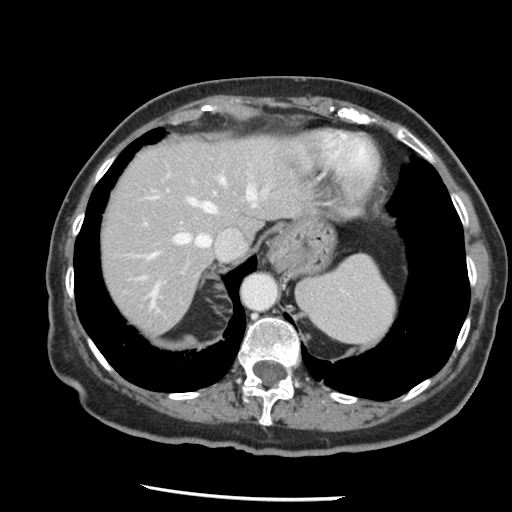
Contrast-enhanced abdominal CT, one axial slice; position 109 of 148 along the scan axis; intravenous contrast given; soft-tissue window (W 400 / L 40 HU); 2.5 mm slice thickness; 512 × 512 image matrix, field of view 330 × 330 mm. Female patient, age 85 years. Case-level facts recorded for this patient, not image findings: diagnosis: colorectal cancer liver metastases, imaged before liver resection; multiple liver metastases: no; largest metastasis: 0.9 cm; disease in both lobes: no.
Annotated regions visible in this slice (manually delineated by an expert):
- hepatic veins: box from (x=146, y=163) to (x=268, y=307) px
- liver: (x=100, y=134)–(x=314, y=334)
- planned liver remnant (the part of the liver to remain after resection): (x=100, y=134)–(x=314, y=334)
- portal vein (with intrahepatic branches): (x=137, y=190)–(x=217, y=280)